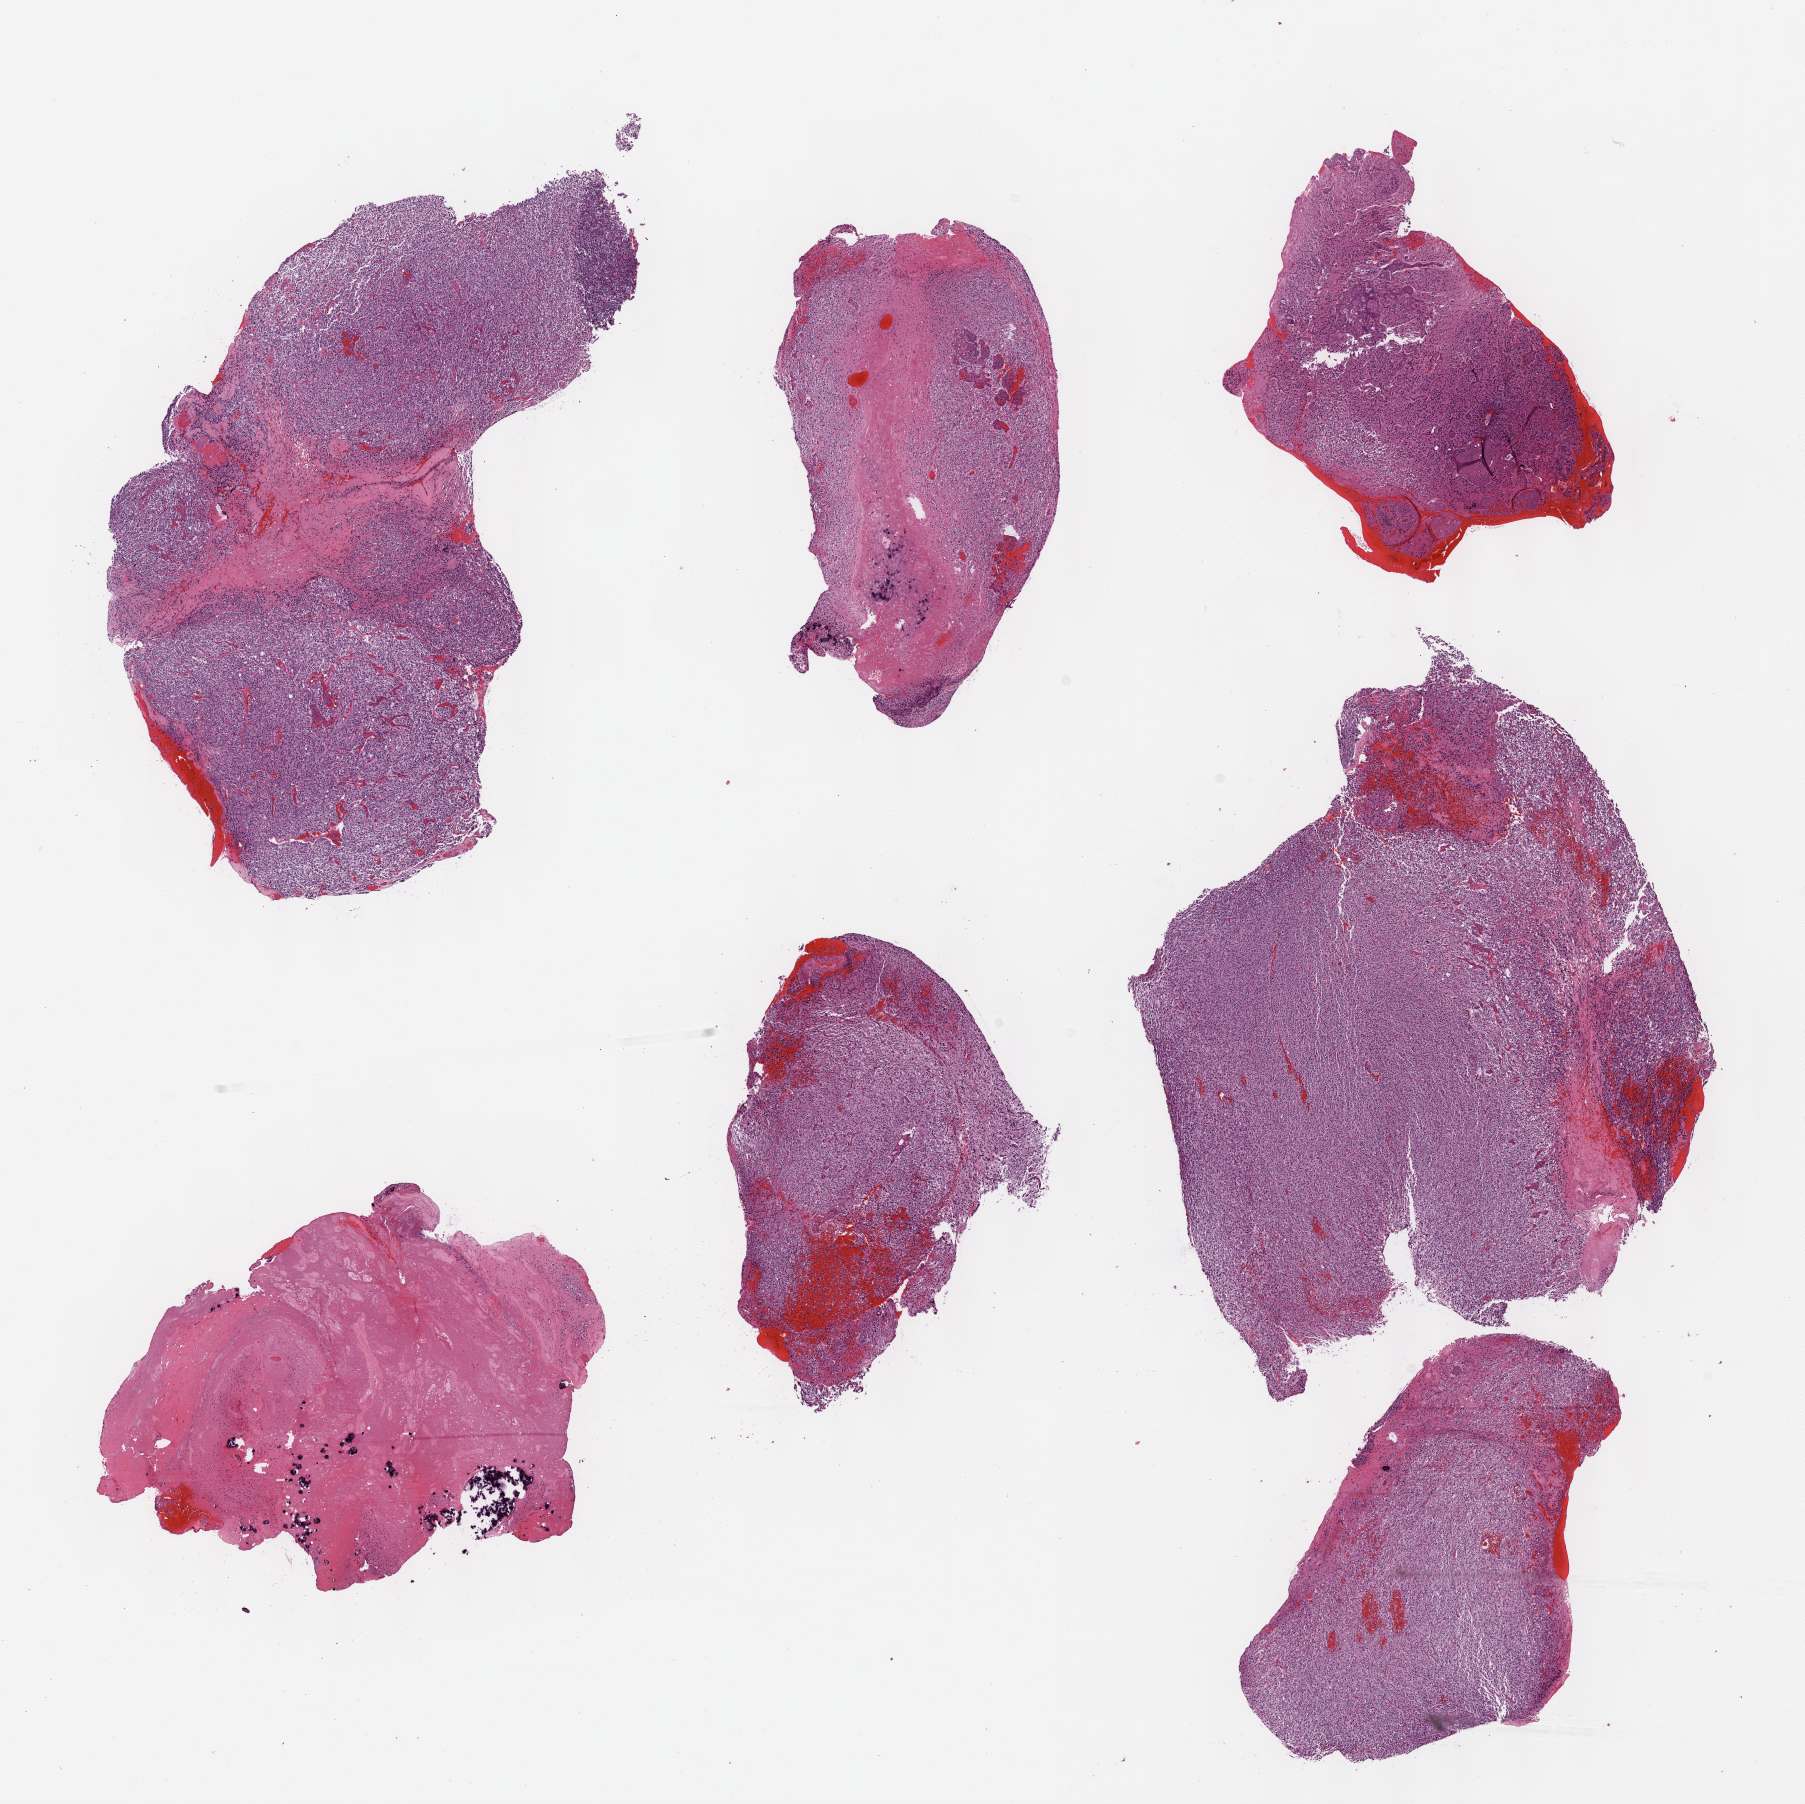
Whole-slide histology image, H&E, whole scanned area (about 14.6 x 14.6 mm) shown as a low-resolution overview, formalin-fixed paraffin-embedded (FFPE) diagnostic section, sample: primary tumour, brain. Patient: female, age at initial diagnosis 58 years. Histologic grade: G3 (poorly differentiated).
Diagnosis: Oligodendroglioma, anaplastic (cerebrum). Laterality: right.